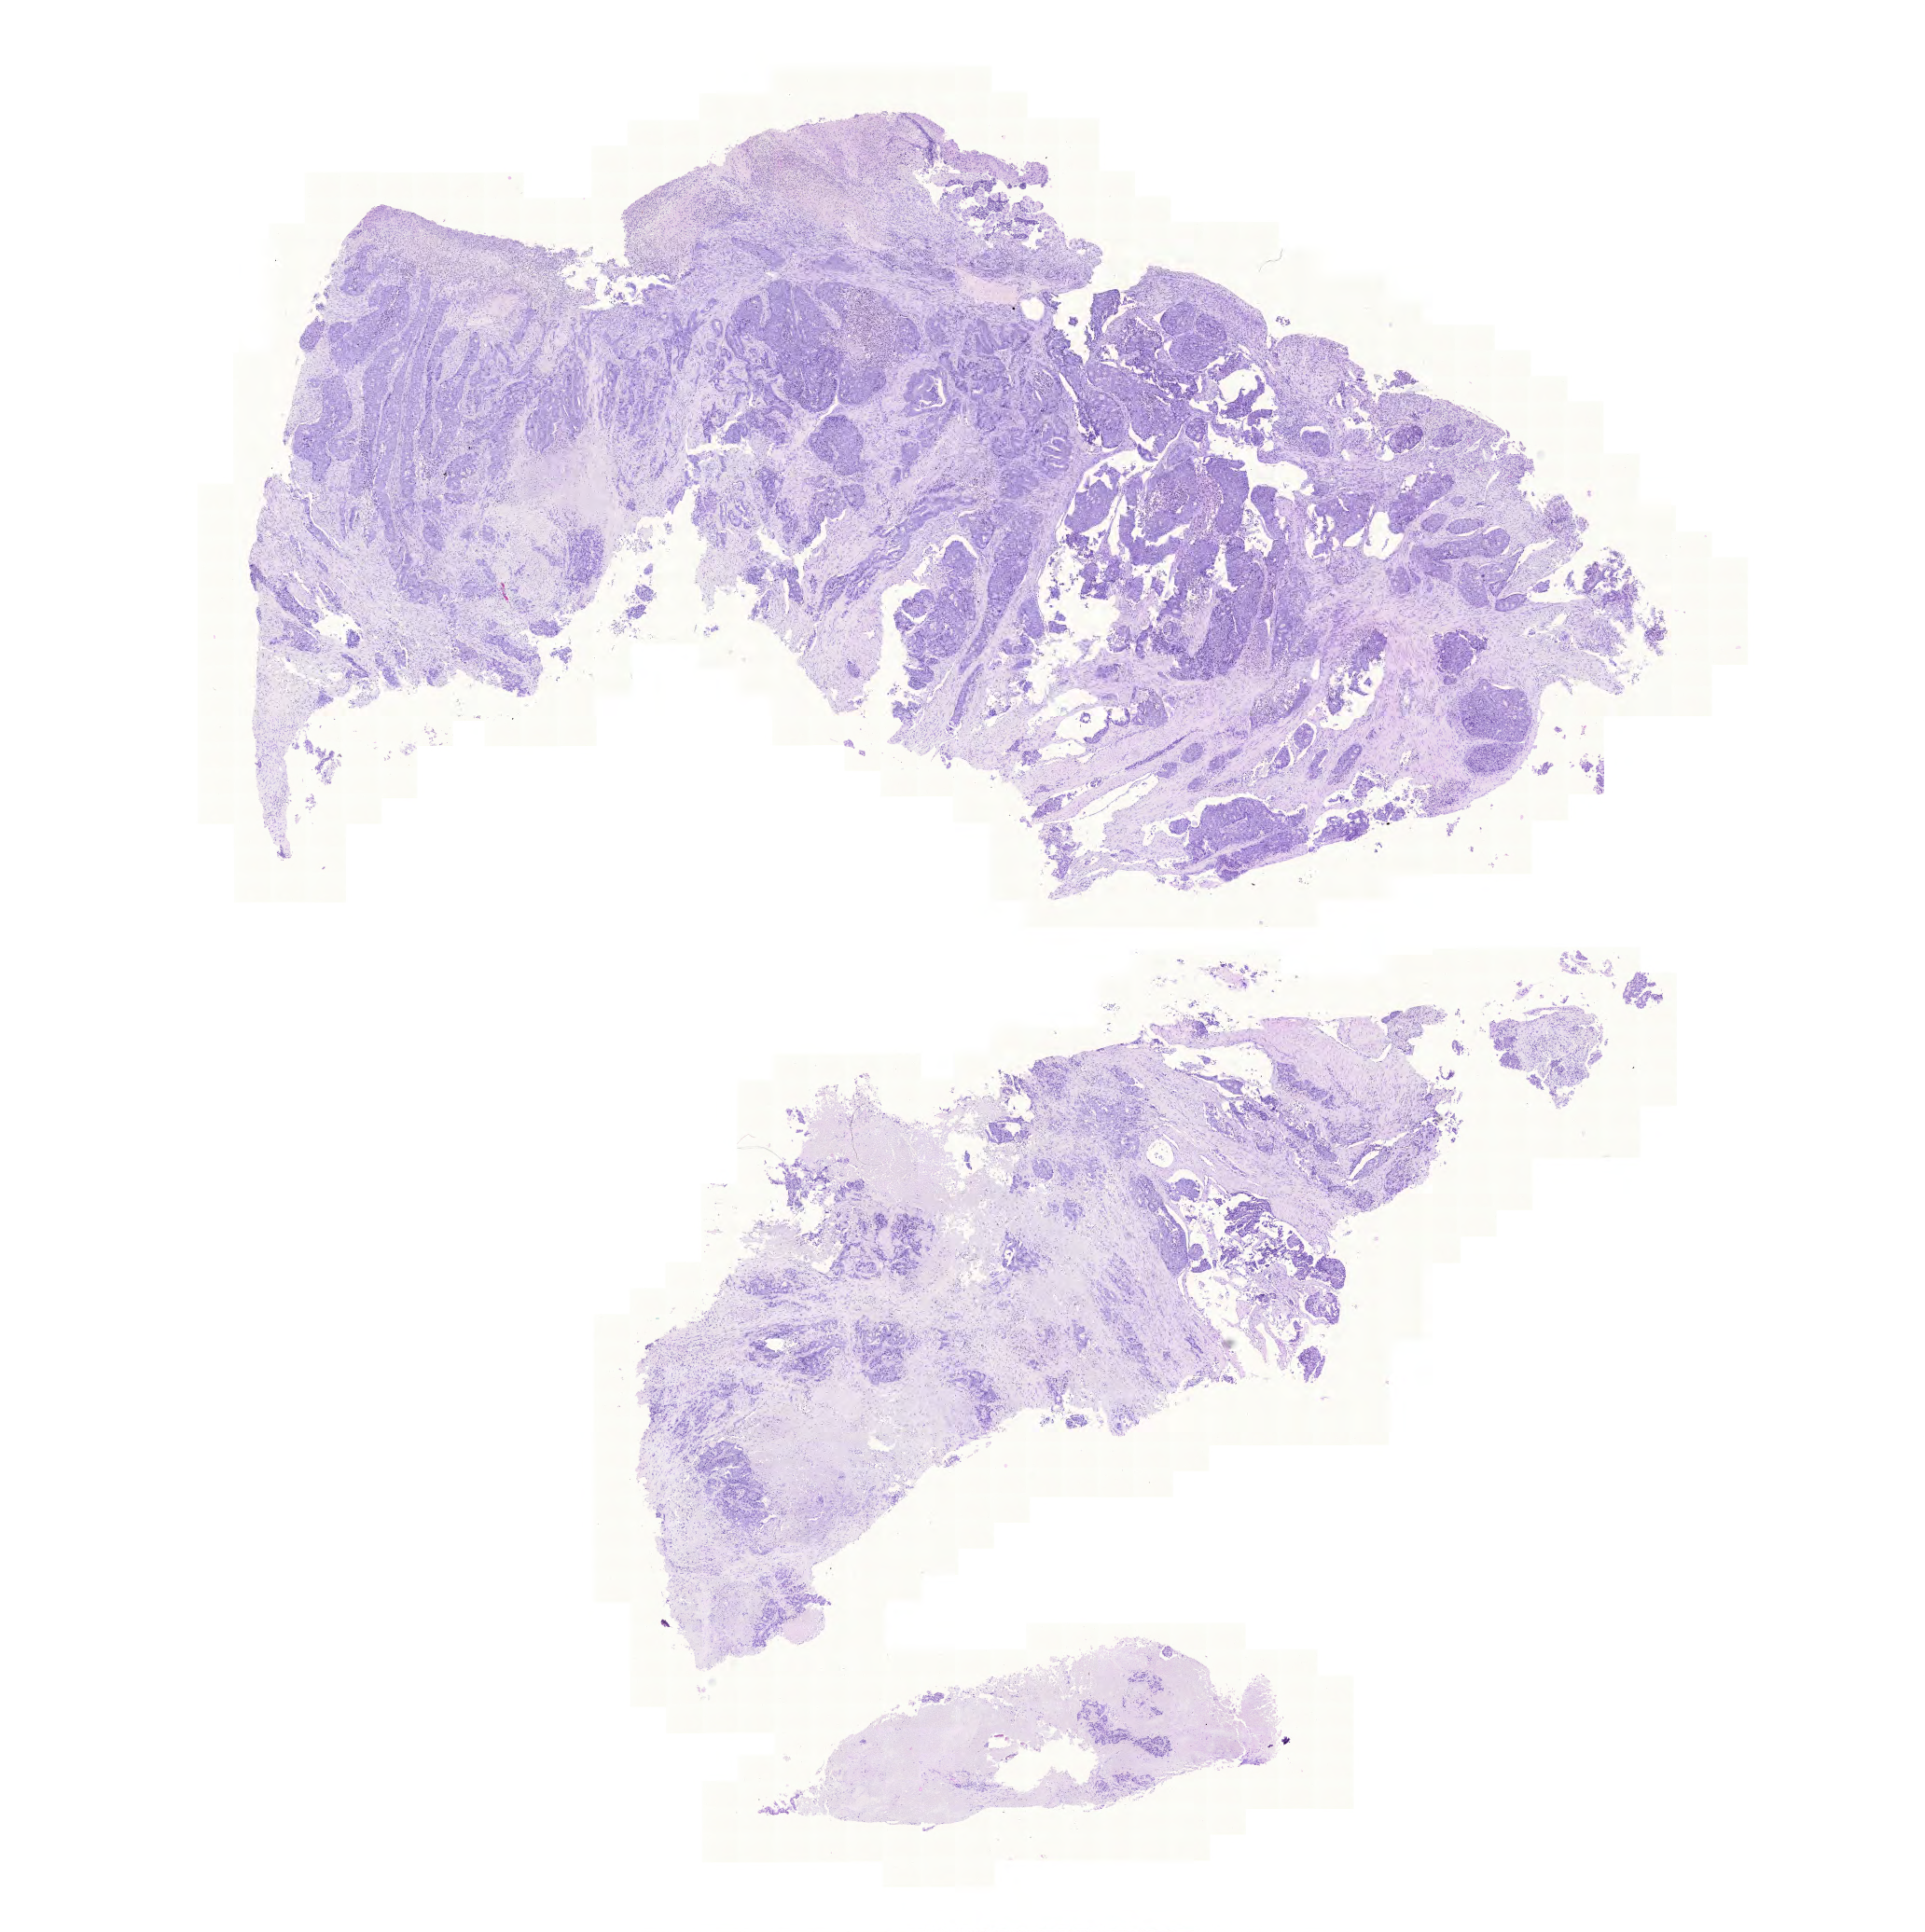
Digitized H&E tissue section (whole slide) — a low-resolution overview of the entire scanned area, about 15.4 x 15.4 mm (acquisition: 20x scan); formalin-fixed paraffin-embedded (FFPE) diagnostic section; sample: primary tumour, rectum. Patient: female, age at initial diagnosis 84 years.
Pathologic diagnosis: Adenocarcinoma, NOS.